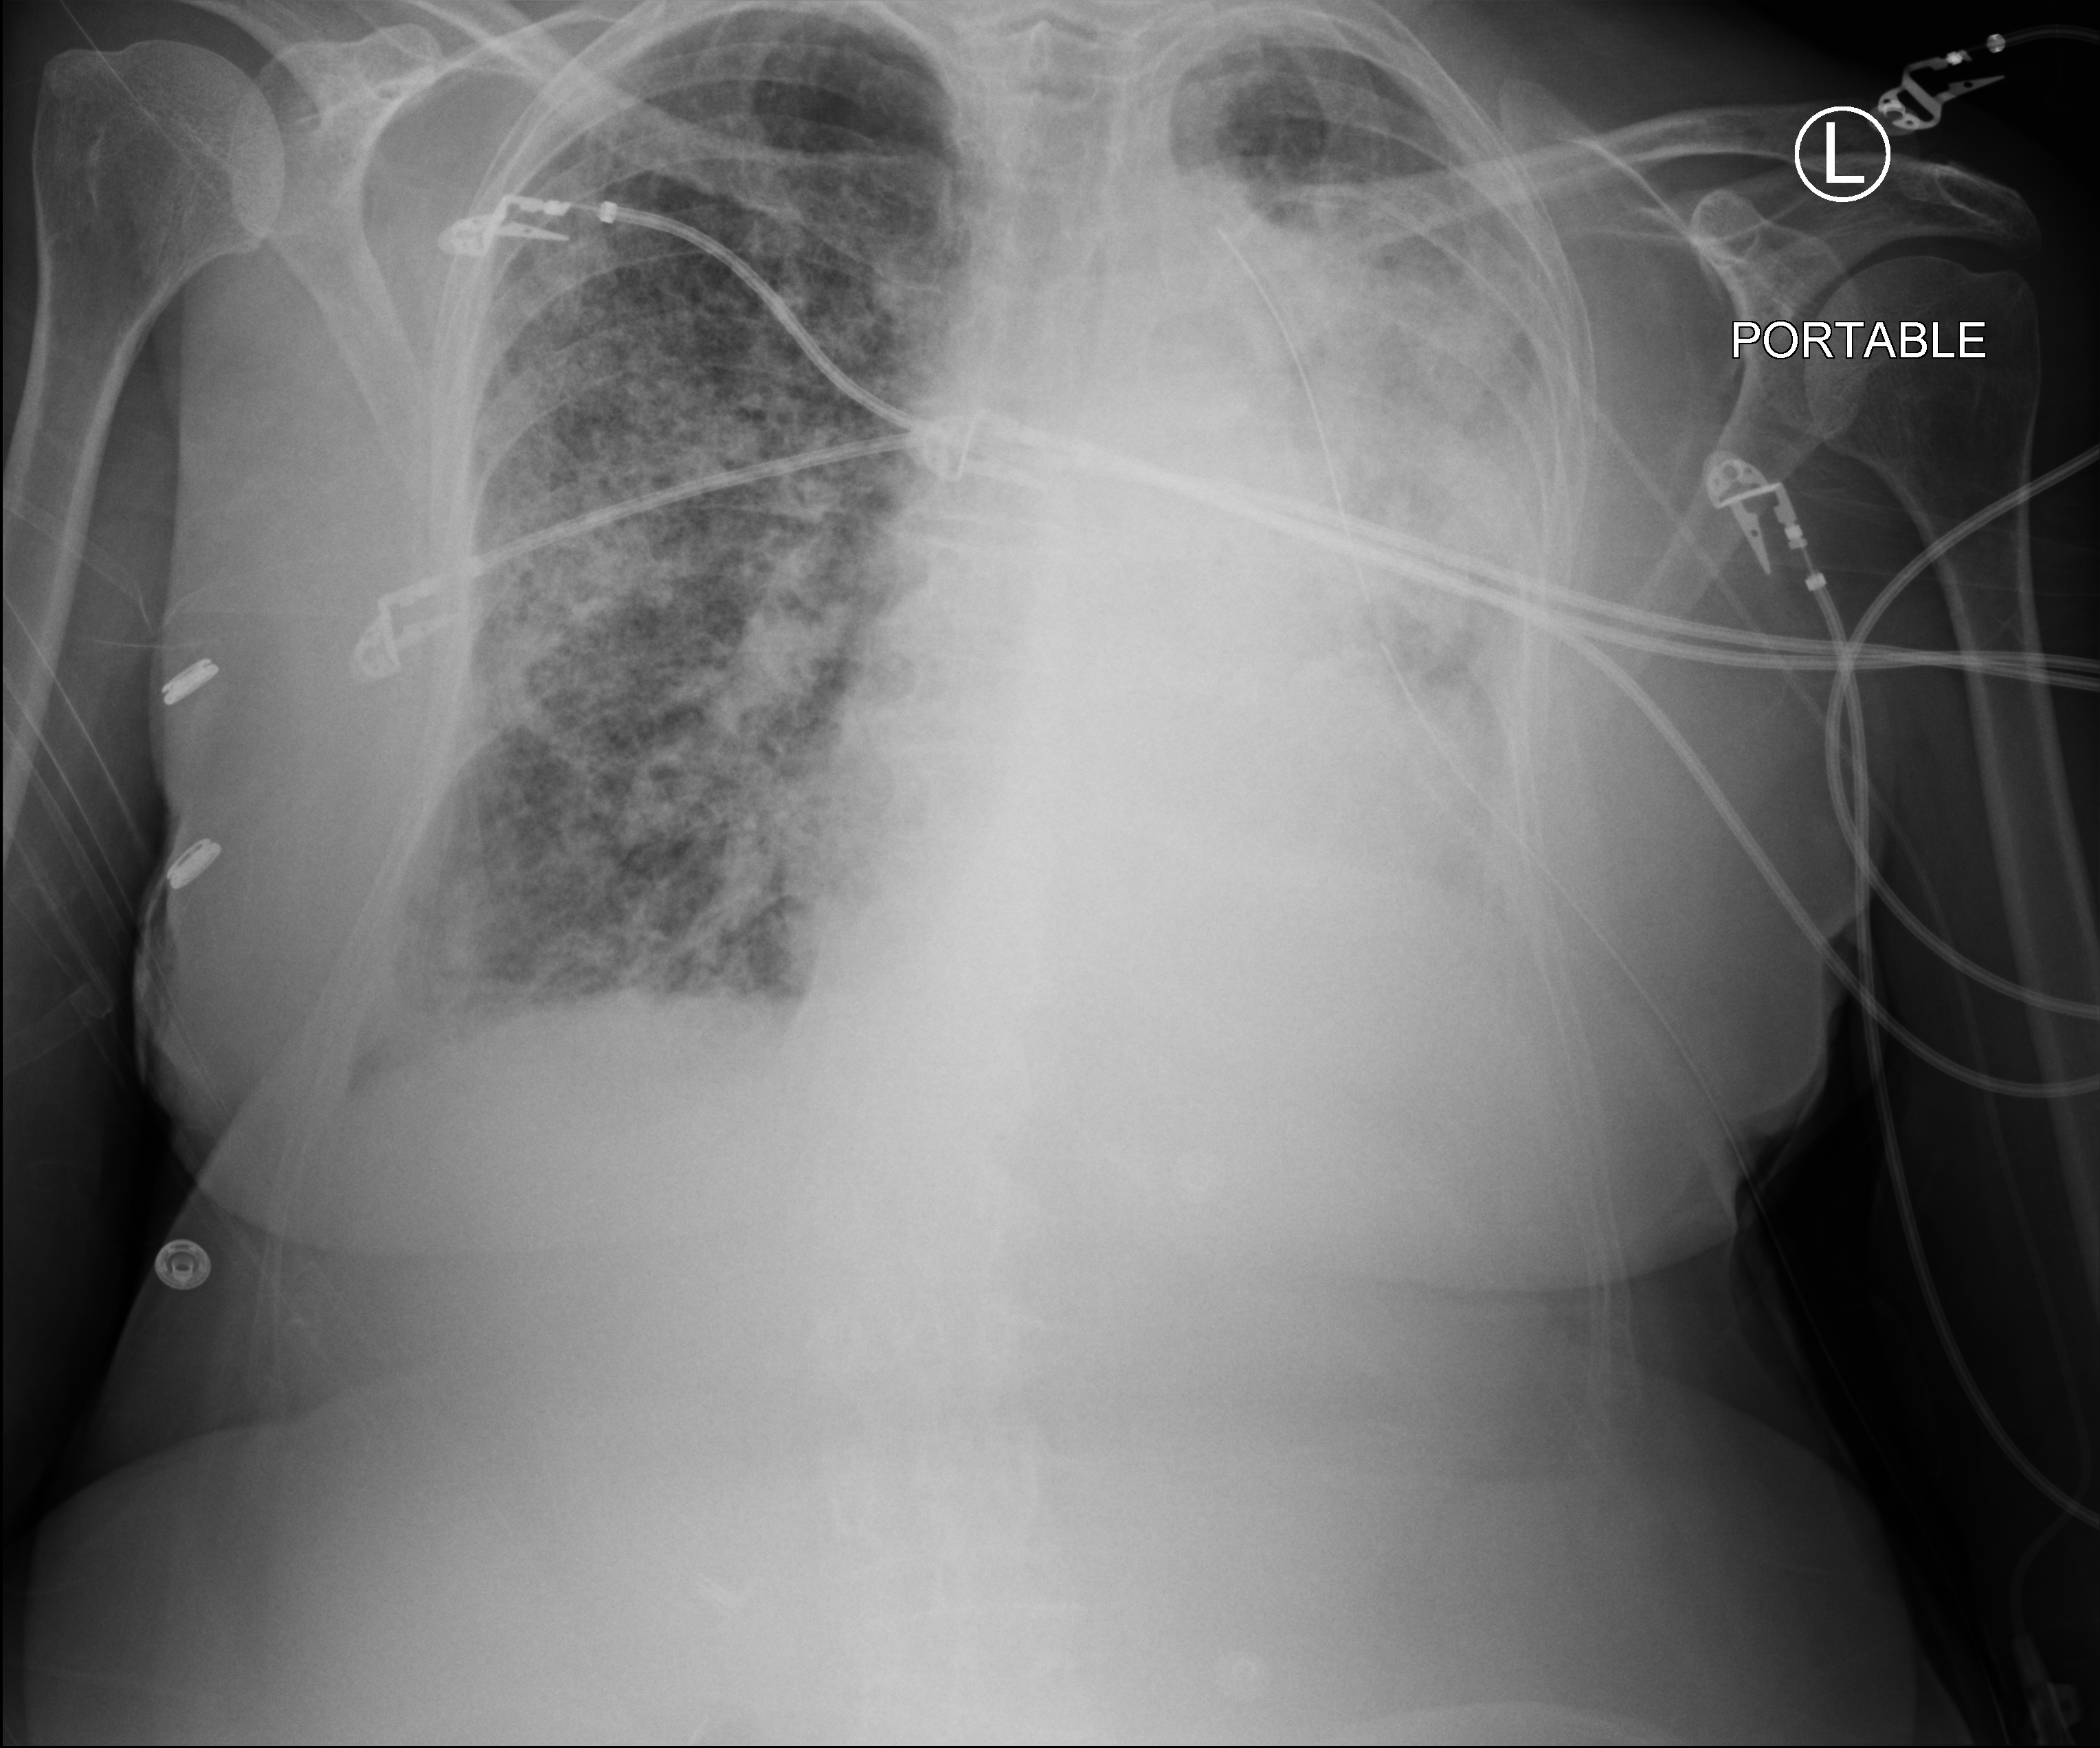
Bedside chest radiograph (computed radiography), anteroposterior (AP) projection. Patient hospitalised with COVID-19; female, aged 75–90 years.
From the hospital-stay record, not from the radiograph (when in the stay this image was taken is not recorded): admitted to intensive care during this hospital stay: yes; mechanically ventilated during this hospital stay: yes; diabetes (admission record): no.